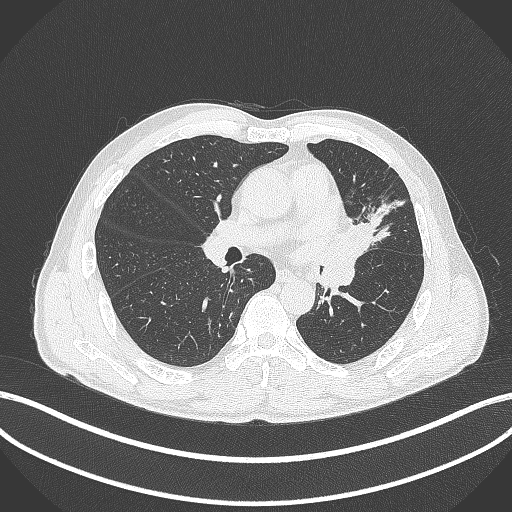
Chest CT, one axial slice; position 229 of 429 along the scan axis; 120 kVp; lung window (W 1500 / L -600 HU); 1 mm slice thickness; 512 × 512 image matrix, field of view 400 × 400 mm. Male patient, age 57 years. Case-level facts recorded for this patient, not image findings: clinical TNM (as recorded): T2b N0 M0.
Structures marked on this image (rectangle marked by the reading radiologist):
- lung tumour (recorded histology: squamous cell carcinoma): bounding box [x1, y1, x2, y2] px = [342, 218, 378, 273]